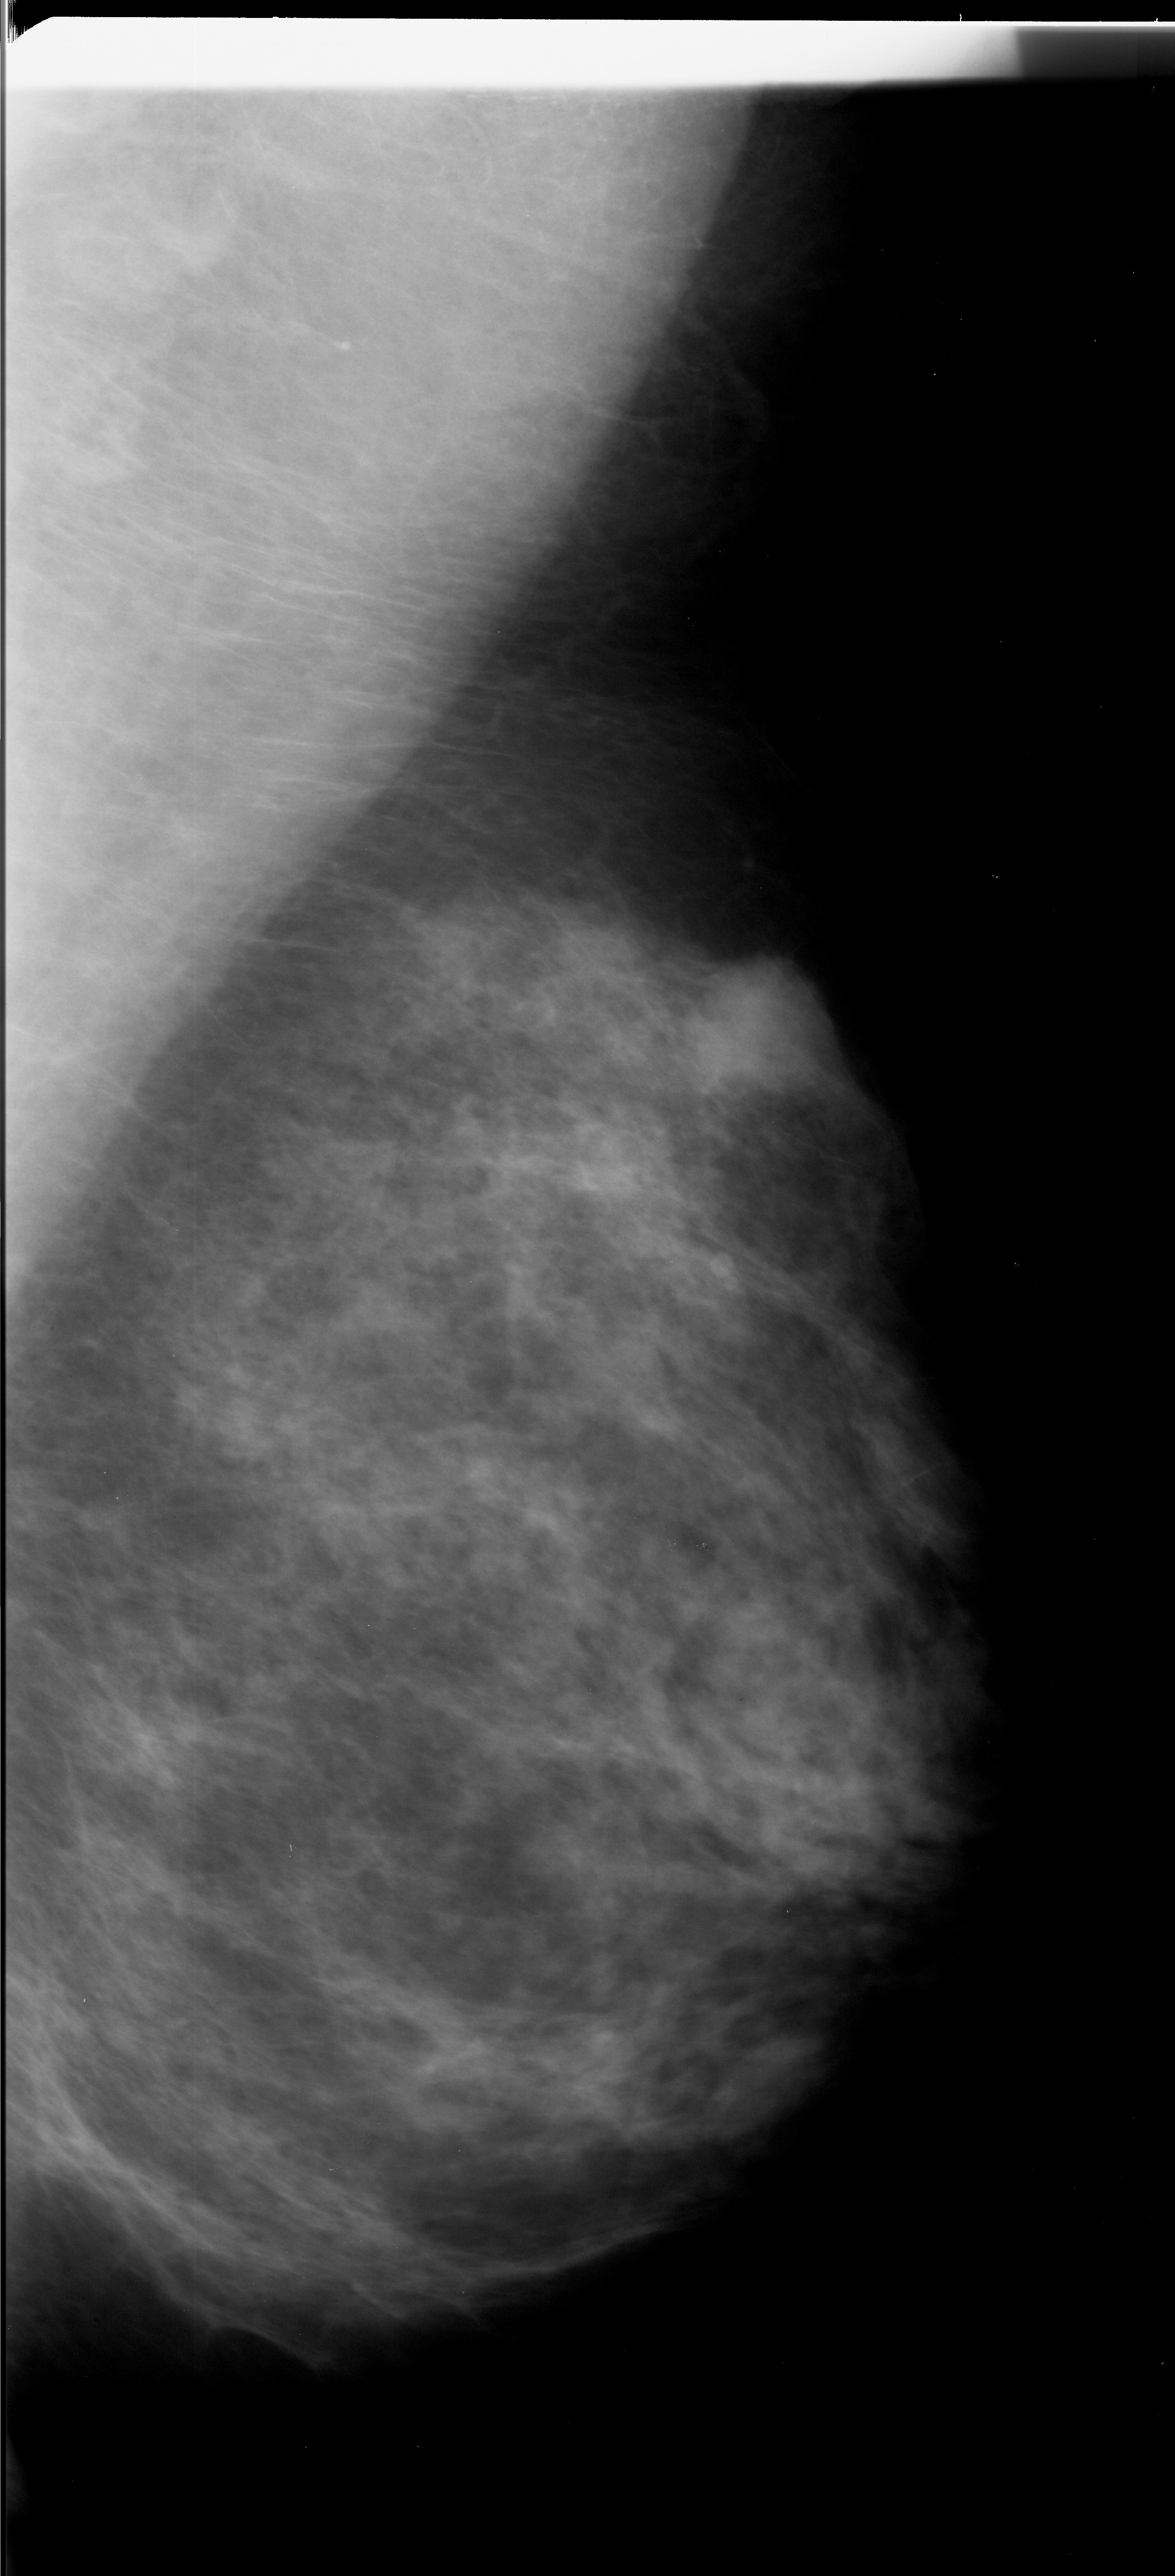
Digitized screen-film mammogram, right breast, MLO view, BI-RADS breast density category 3 (scale 1–4).
Finding: mass, shape irregular, margins ill defined; BI-RADS assessment category 4; subtlety rating 4 on a 1 (subtle) to 5 (obvious) scale; pathology result (as recorded, not read from the image): malignant.